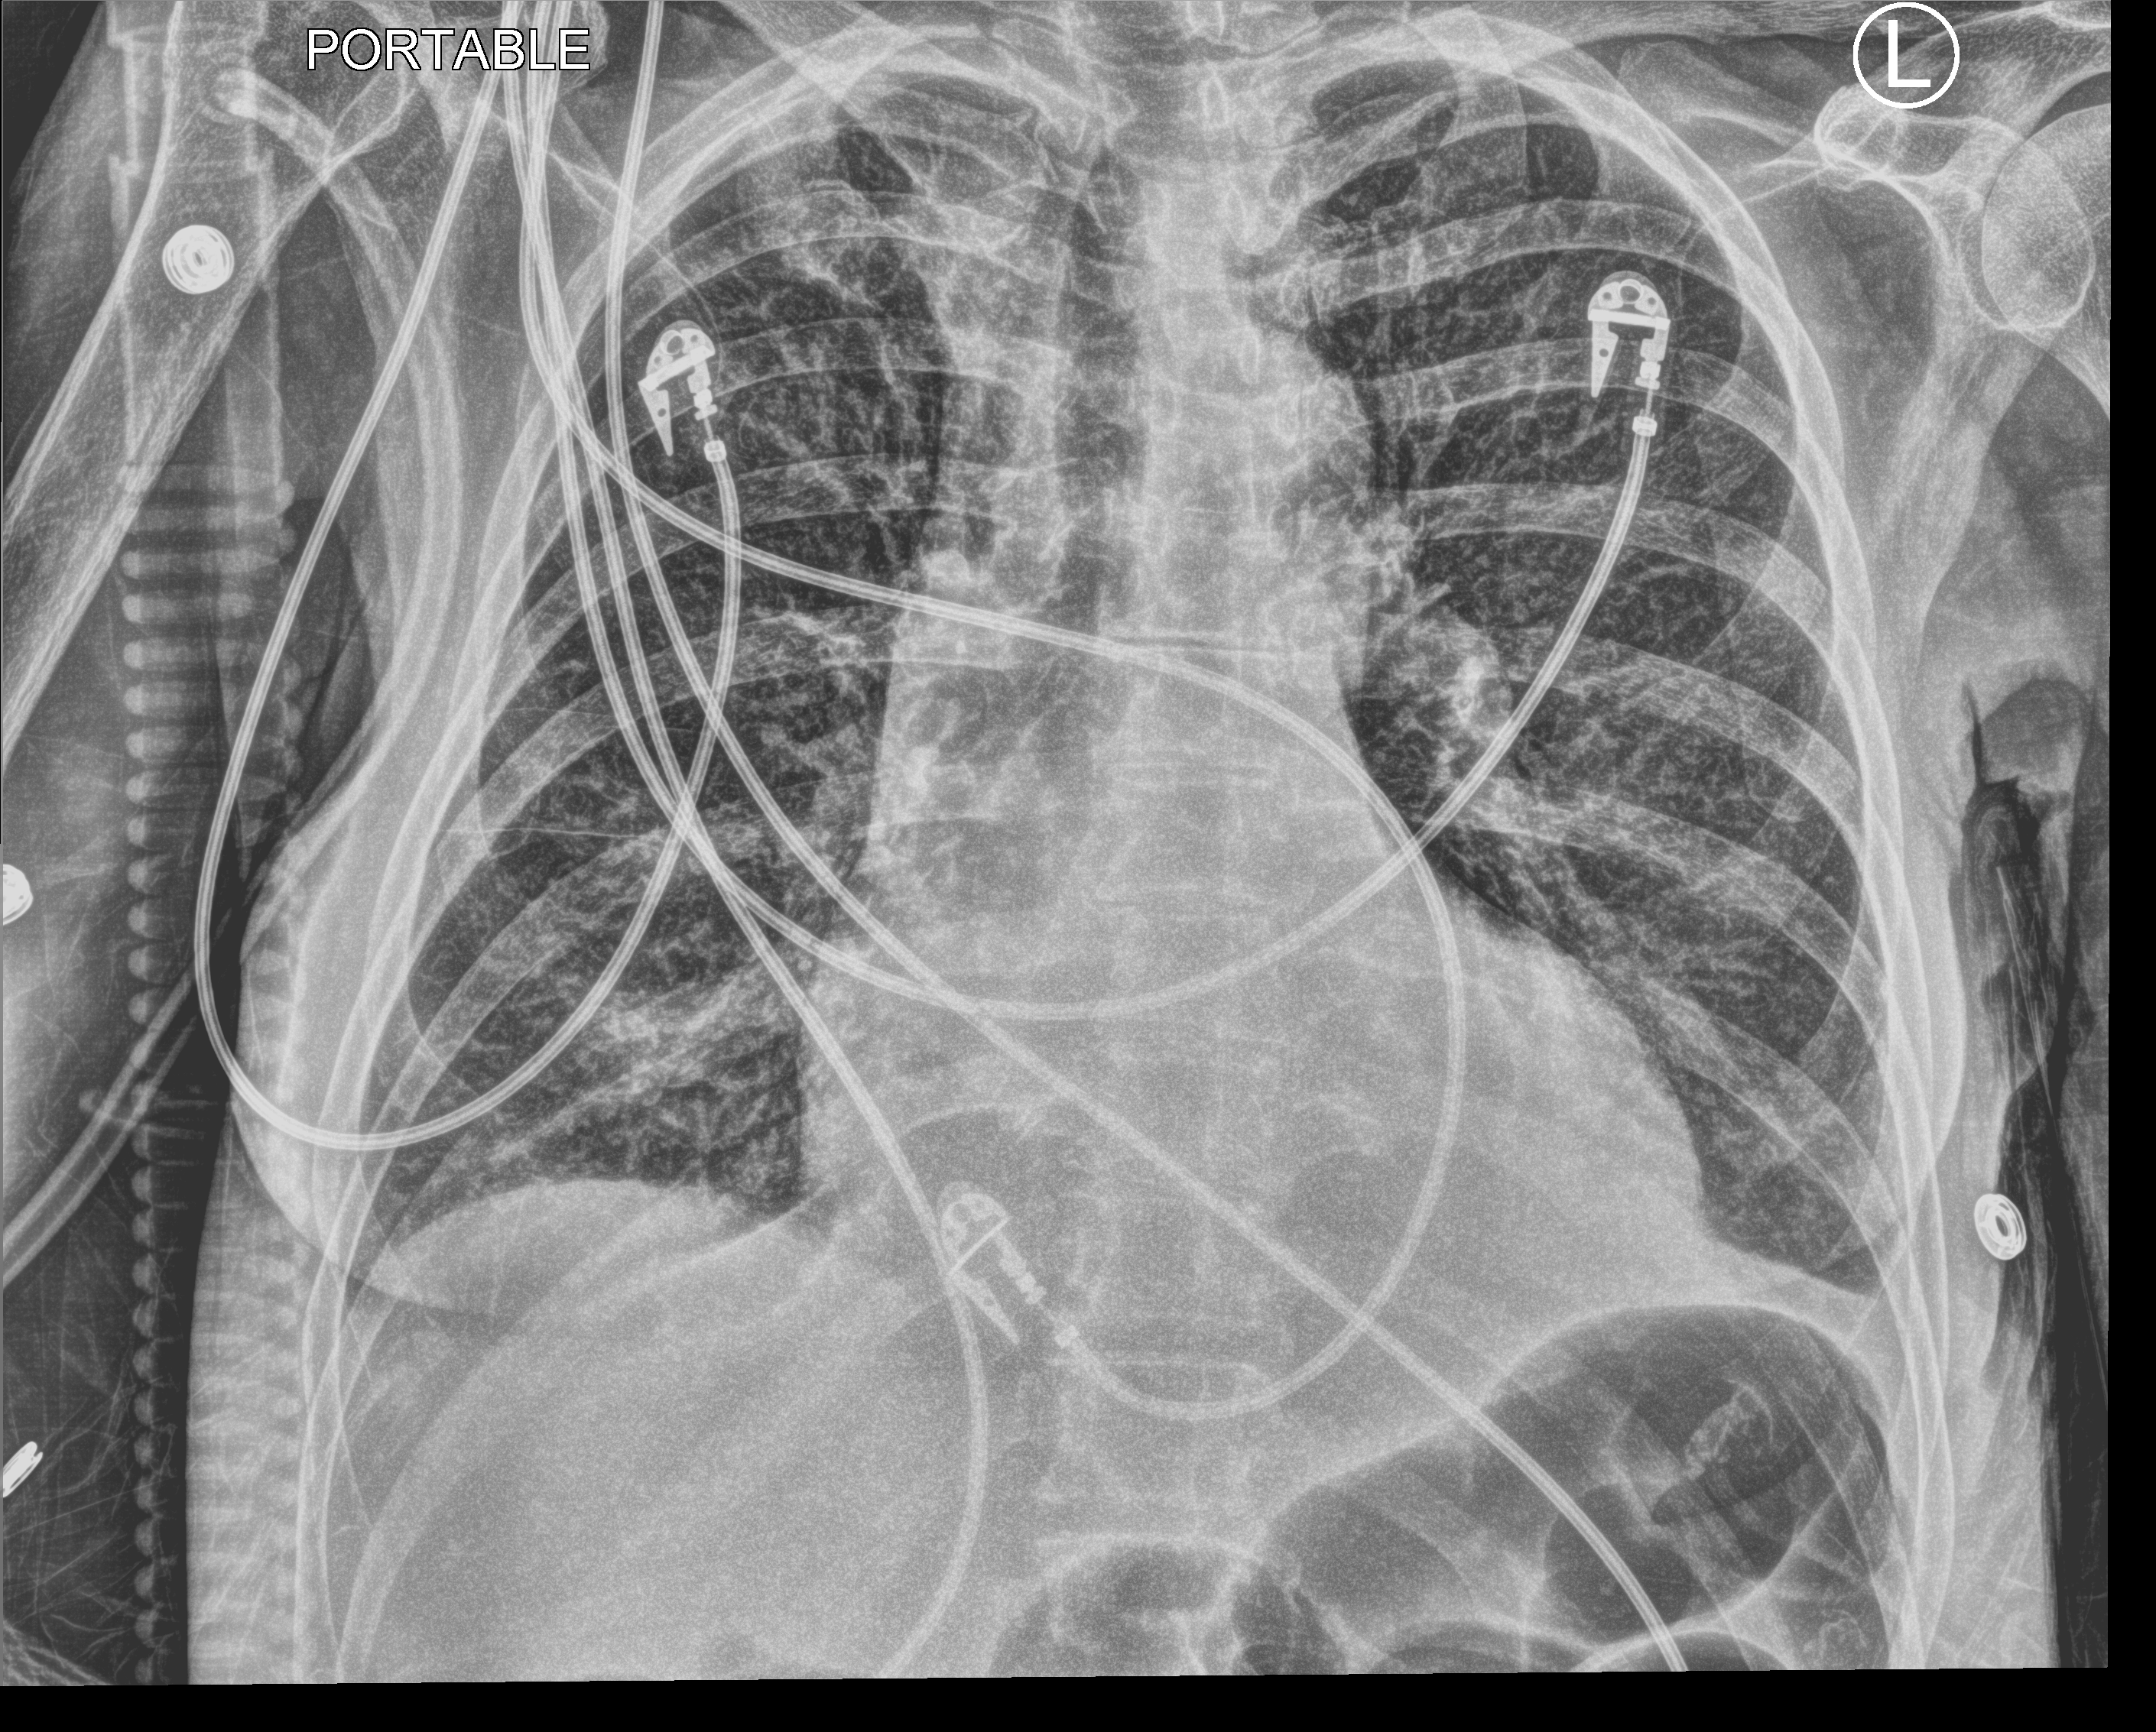
Portable chest radiograph; anteroposterior (AP) projection. Patient hospitalised with COVID-19; female, aged 60–74 years.
Hospital-stay facts (about this admission, not read from this image; timing relative to this image not recorded):
- admitted to intensive care during this hospital stay: yes